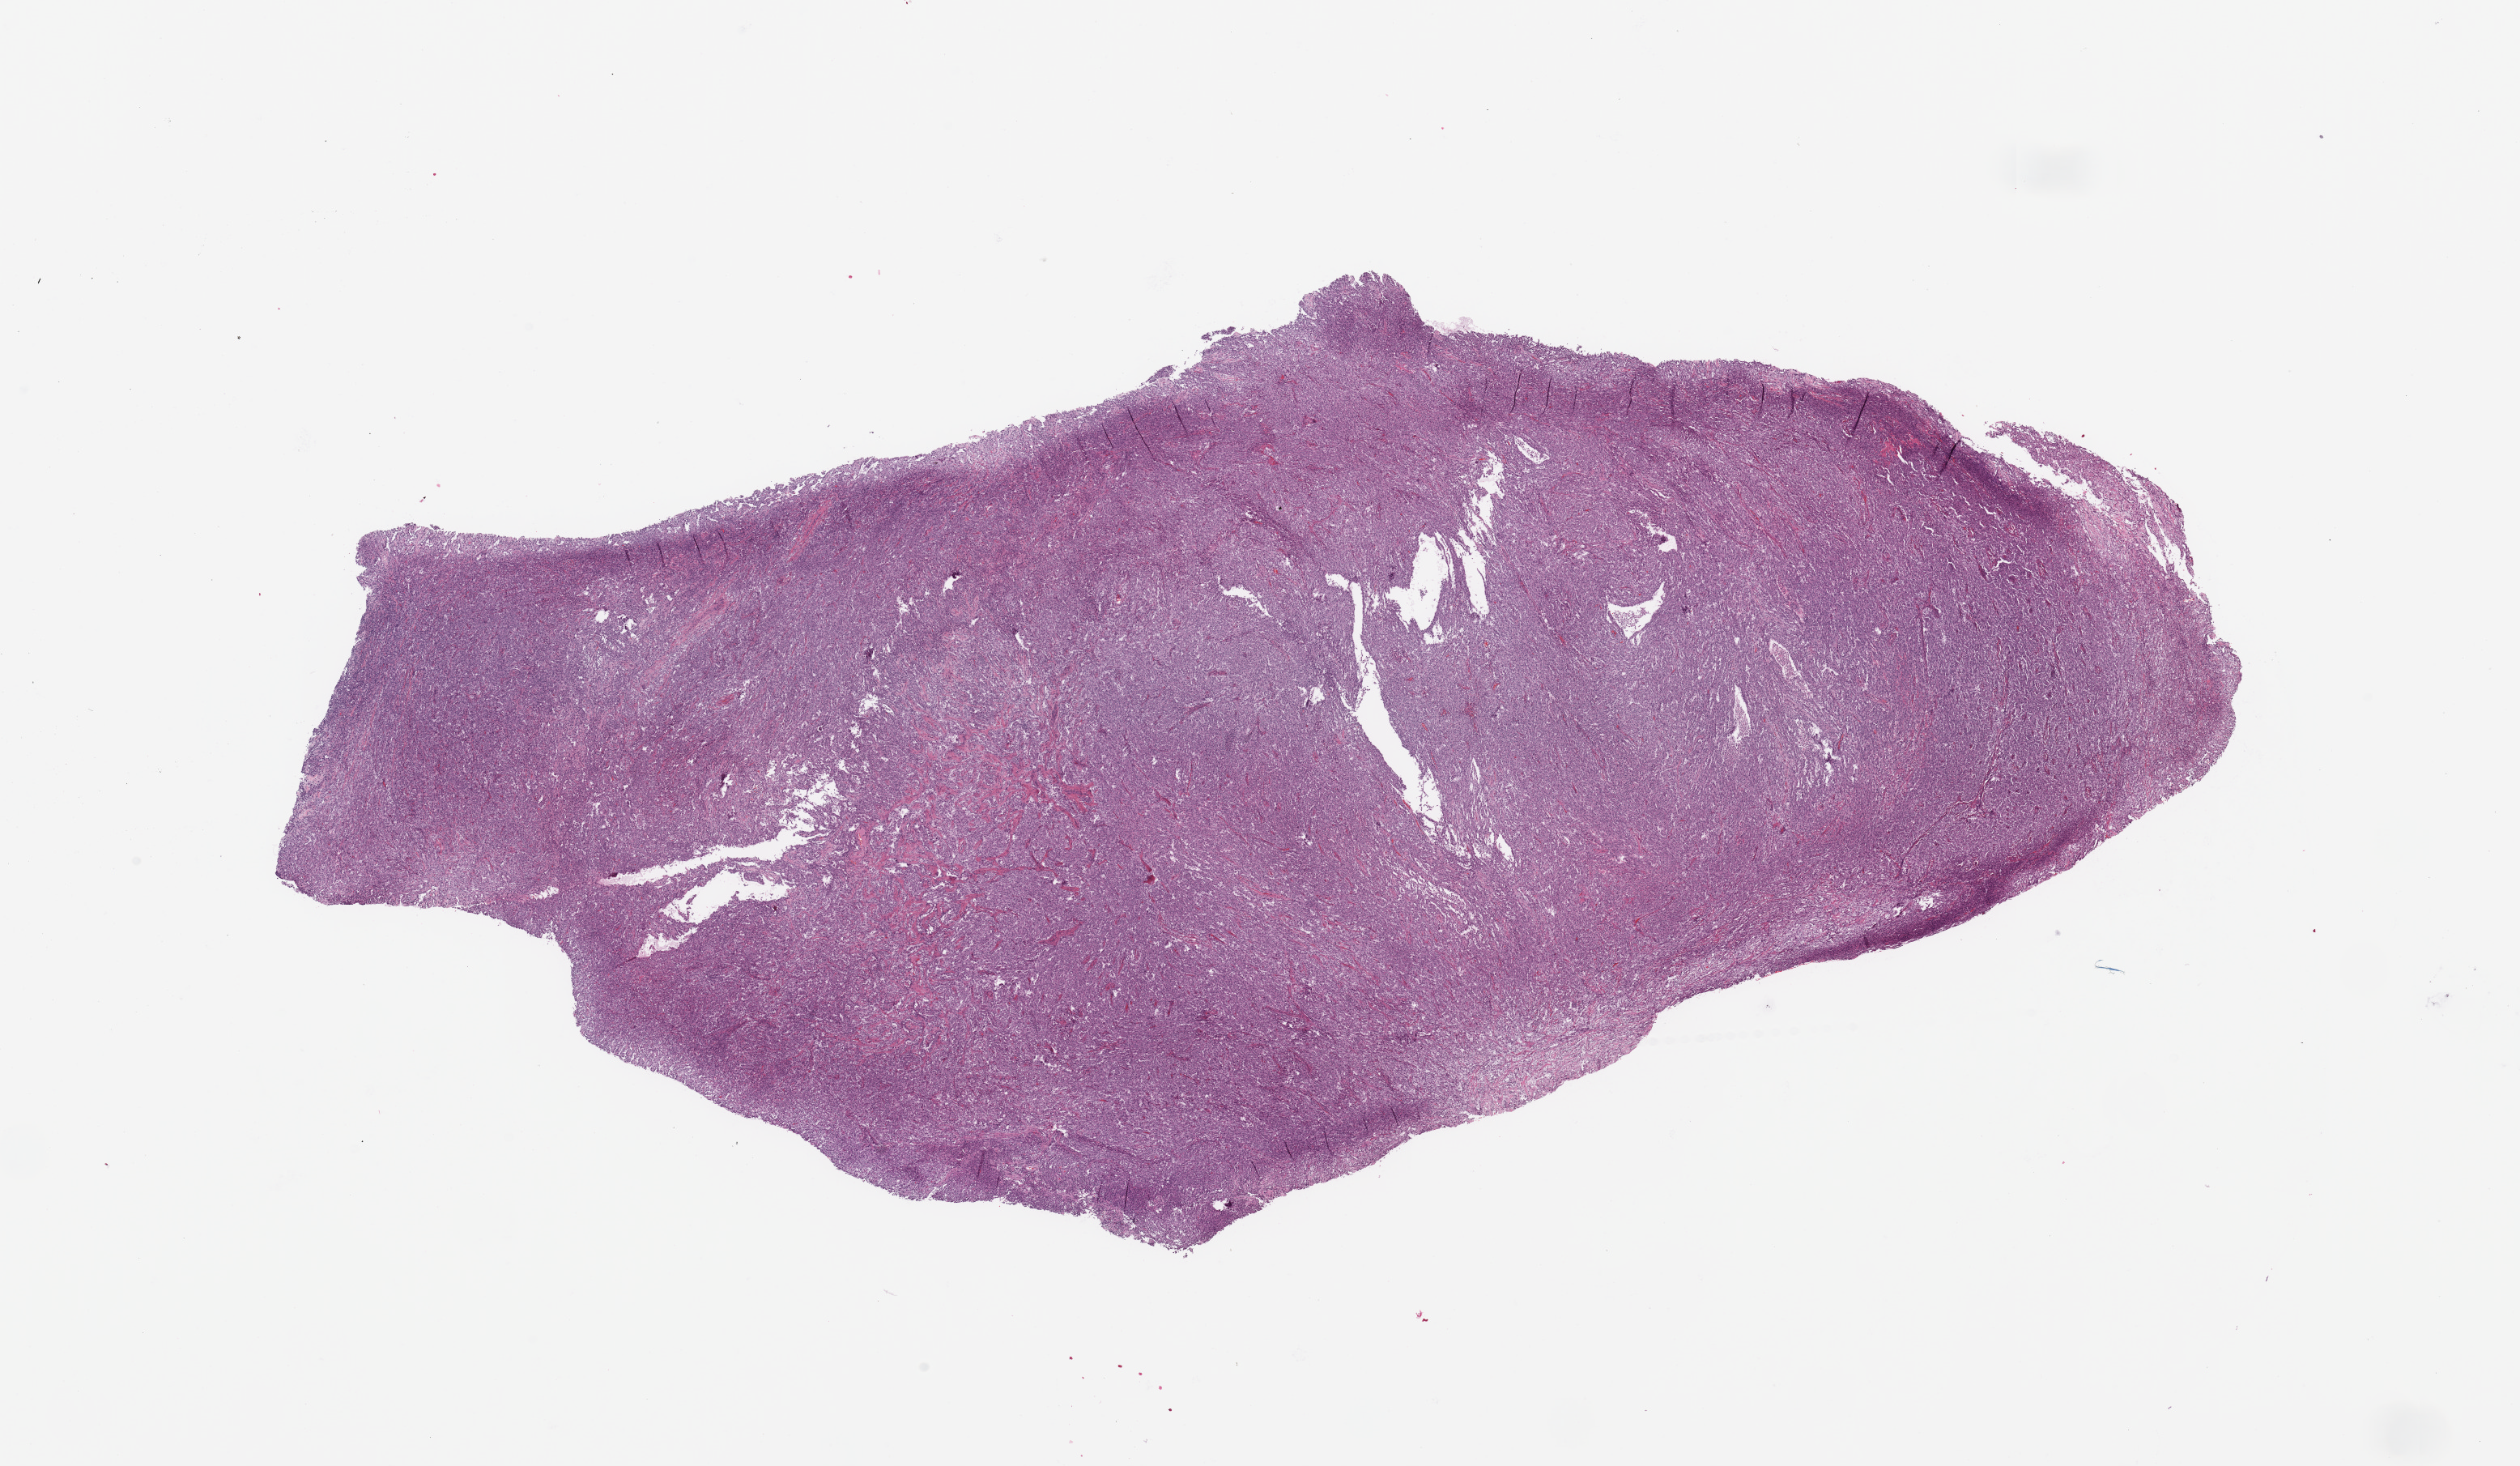
Whole-slide histology image, H&E-stained — low-resolution overview of the scanned area, about 24.6 x 14.3 mm, tumour tissue sample, kidney. 61-year-old male patient. Histologic grade: G4 (undifferentiated).
Histologic diagnosis: Renal cell carcinoma, NOS. Primary tumour site (as recorded): upper pole. AJCC pathologic stage: IV.